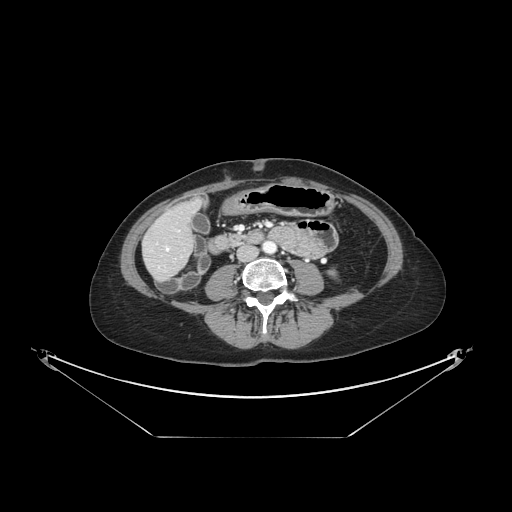
Contrast-enhanced abdominal CT, one axial slice. Position 33 of 148 along the scan axis. 120 kVp. Intravenous contrast given. Soft-tissue window (W 400 / L 40 HU). 2.5 mm slice thickness. 512 × 512 image matrix, field of view 500 × 500 mm. Female patient, age 73 years. Case-level facts recorded for this patient, not image findings: diagnosis: colorectal cancer liver metastases, imaged before liver resection; multiple liver metastases: no; largest metastasis: 1 cm; chemotherapy before resection: yes.
Outlined on this slice (expert manual segmentation):
- hepatic veins: bounding box <166,248,169,251> (left, top, right, bottom; pixels)
- liver: <144,203,198,280>
- planned liver remnant (the part of the liver to remain after resection): <162,203,197,238>